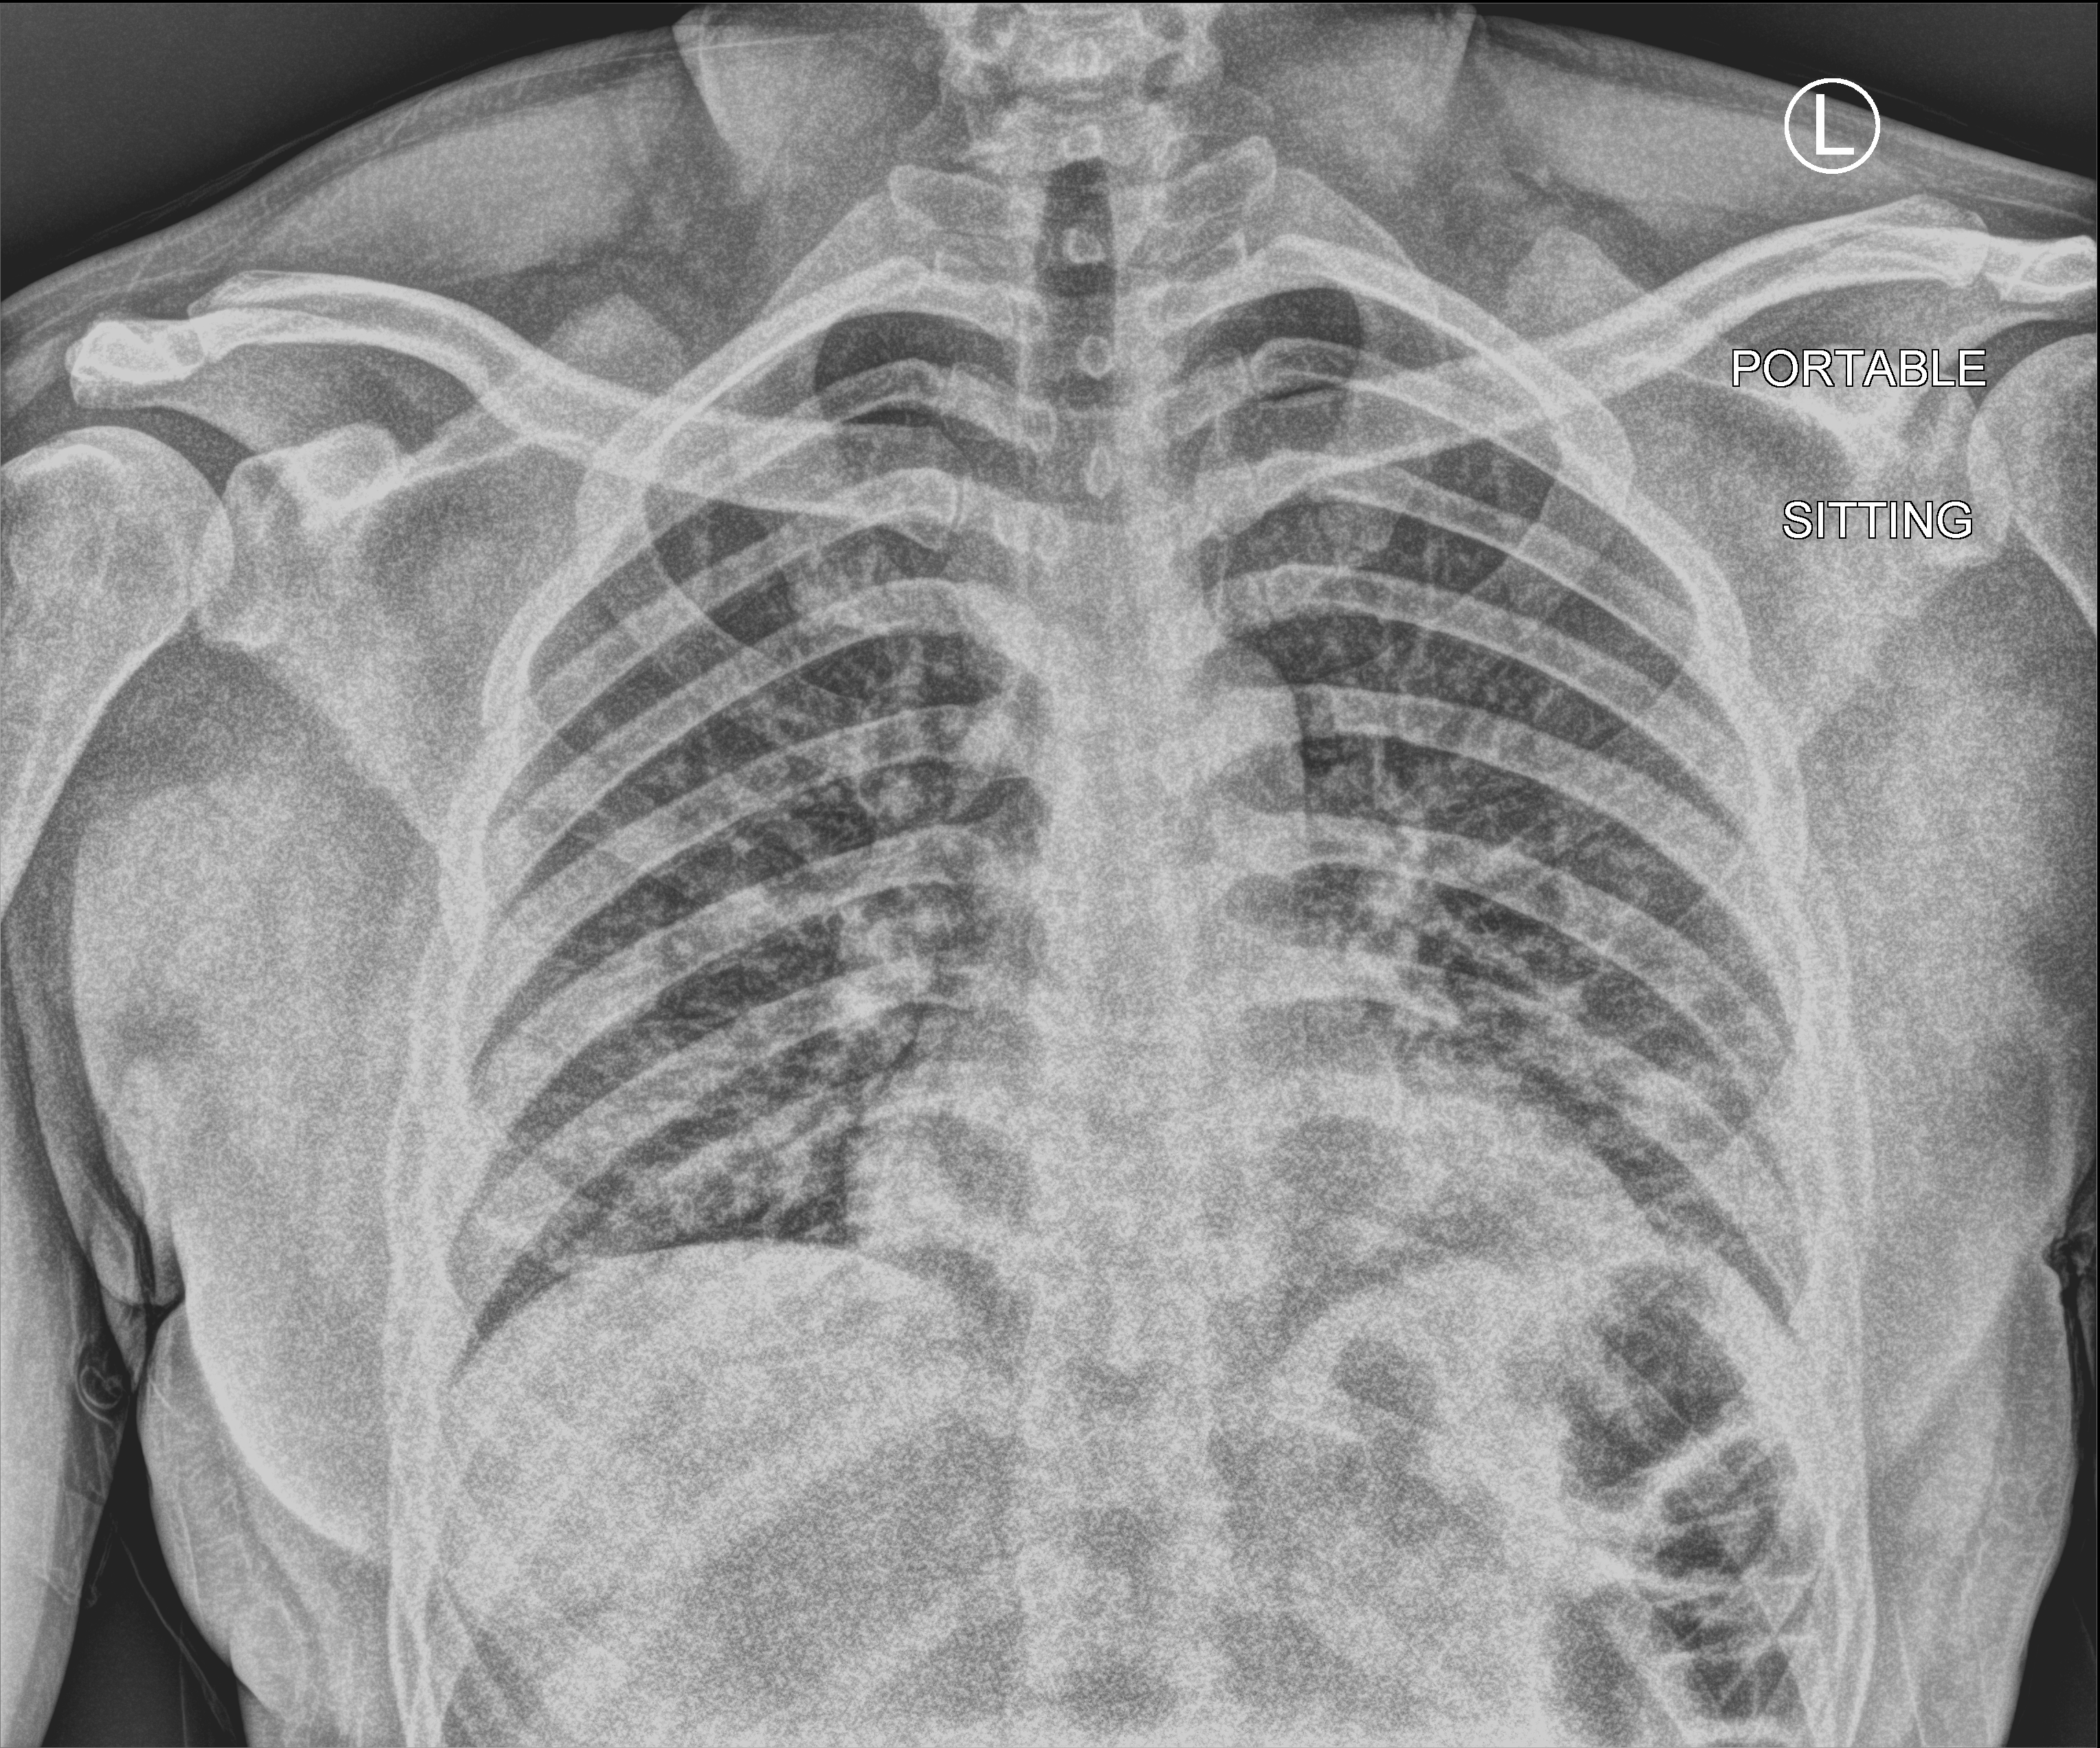
Bedside chest radiograph (computed radiography), anteroposterior (AP) projection. Patient hospitalised with COVID-19; male, aged 18–59 years.
From the hospital-stay record, not from the radiograph (when in the stay this image was taken is not recorded): mechanically ventilated during this hospital stay: no; chronic kidney disease (admission record): no.